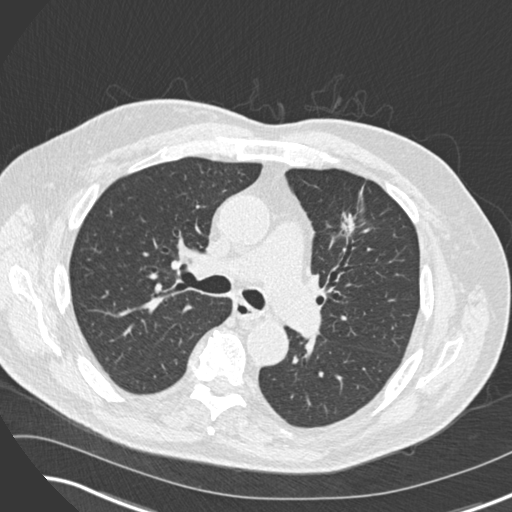
Low-dose screening chest CT, axial slice. Third annual screen. Lung window (W 1500 / L -600 HU). 2 mm slice thickness. Male participant, aged 74 years at enrolment.
• Expert-annotated lung lesion, box from (x=320, y=199) to (x=378, y=250) px.
• Reader record for this screening exam (exam-level; its link to the box is not recorded): non-calcified nodule or mass ≥4 mm, left upper lobe, 12 × 10 mm, spiculated (stellate) margins, soft tissue attenuation, pre-existing on the prior screen: yes; interval growth: yes.
• Later outcome: lung cancer diagnosed 349 days after this screen — adenocarcinoma, NOS, left upper lobe, poorly differentiated (G3), stage IIIA (AJCC 6th edition), 27 mm at pathology.